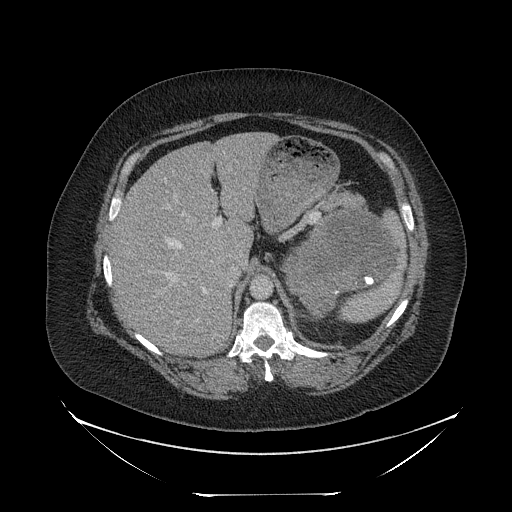
Contrast-enhanced abdominal CT, one axial slice; slice 161 of 205 in the series (ordered by position); reconstruction kernel STANDARD; intravenous contrast given; soft-tissue window (W 400 / L 40 HU); 2.5 mm slice thickness; 512 × 512 image matrix, field of view 500 × 500 mm. Female patient, age 53 years. From the clinical record (not read from this slice): diagnosis: adrenocortical carcinoma; tumour side: left adrenal; tumour size at pathology: 17 cm; Ki-67 index: 20 %.
Outlined on this slice (semi-automatic segmentation, software-assisted and operator-edited):
- mass: box from (x=281, y=215) to (x=393, y=315) px